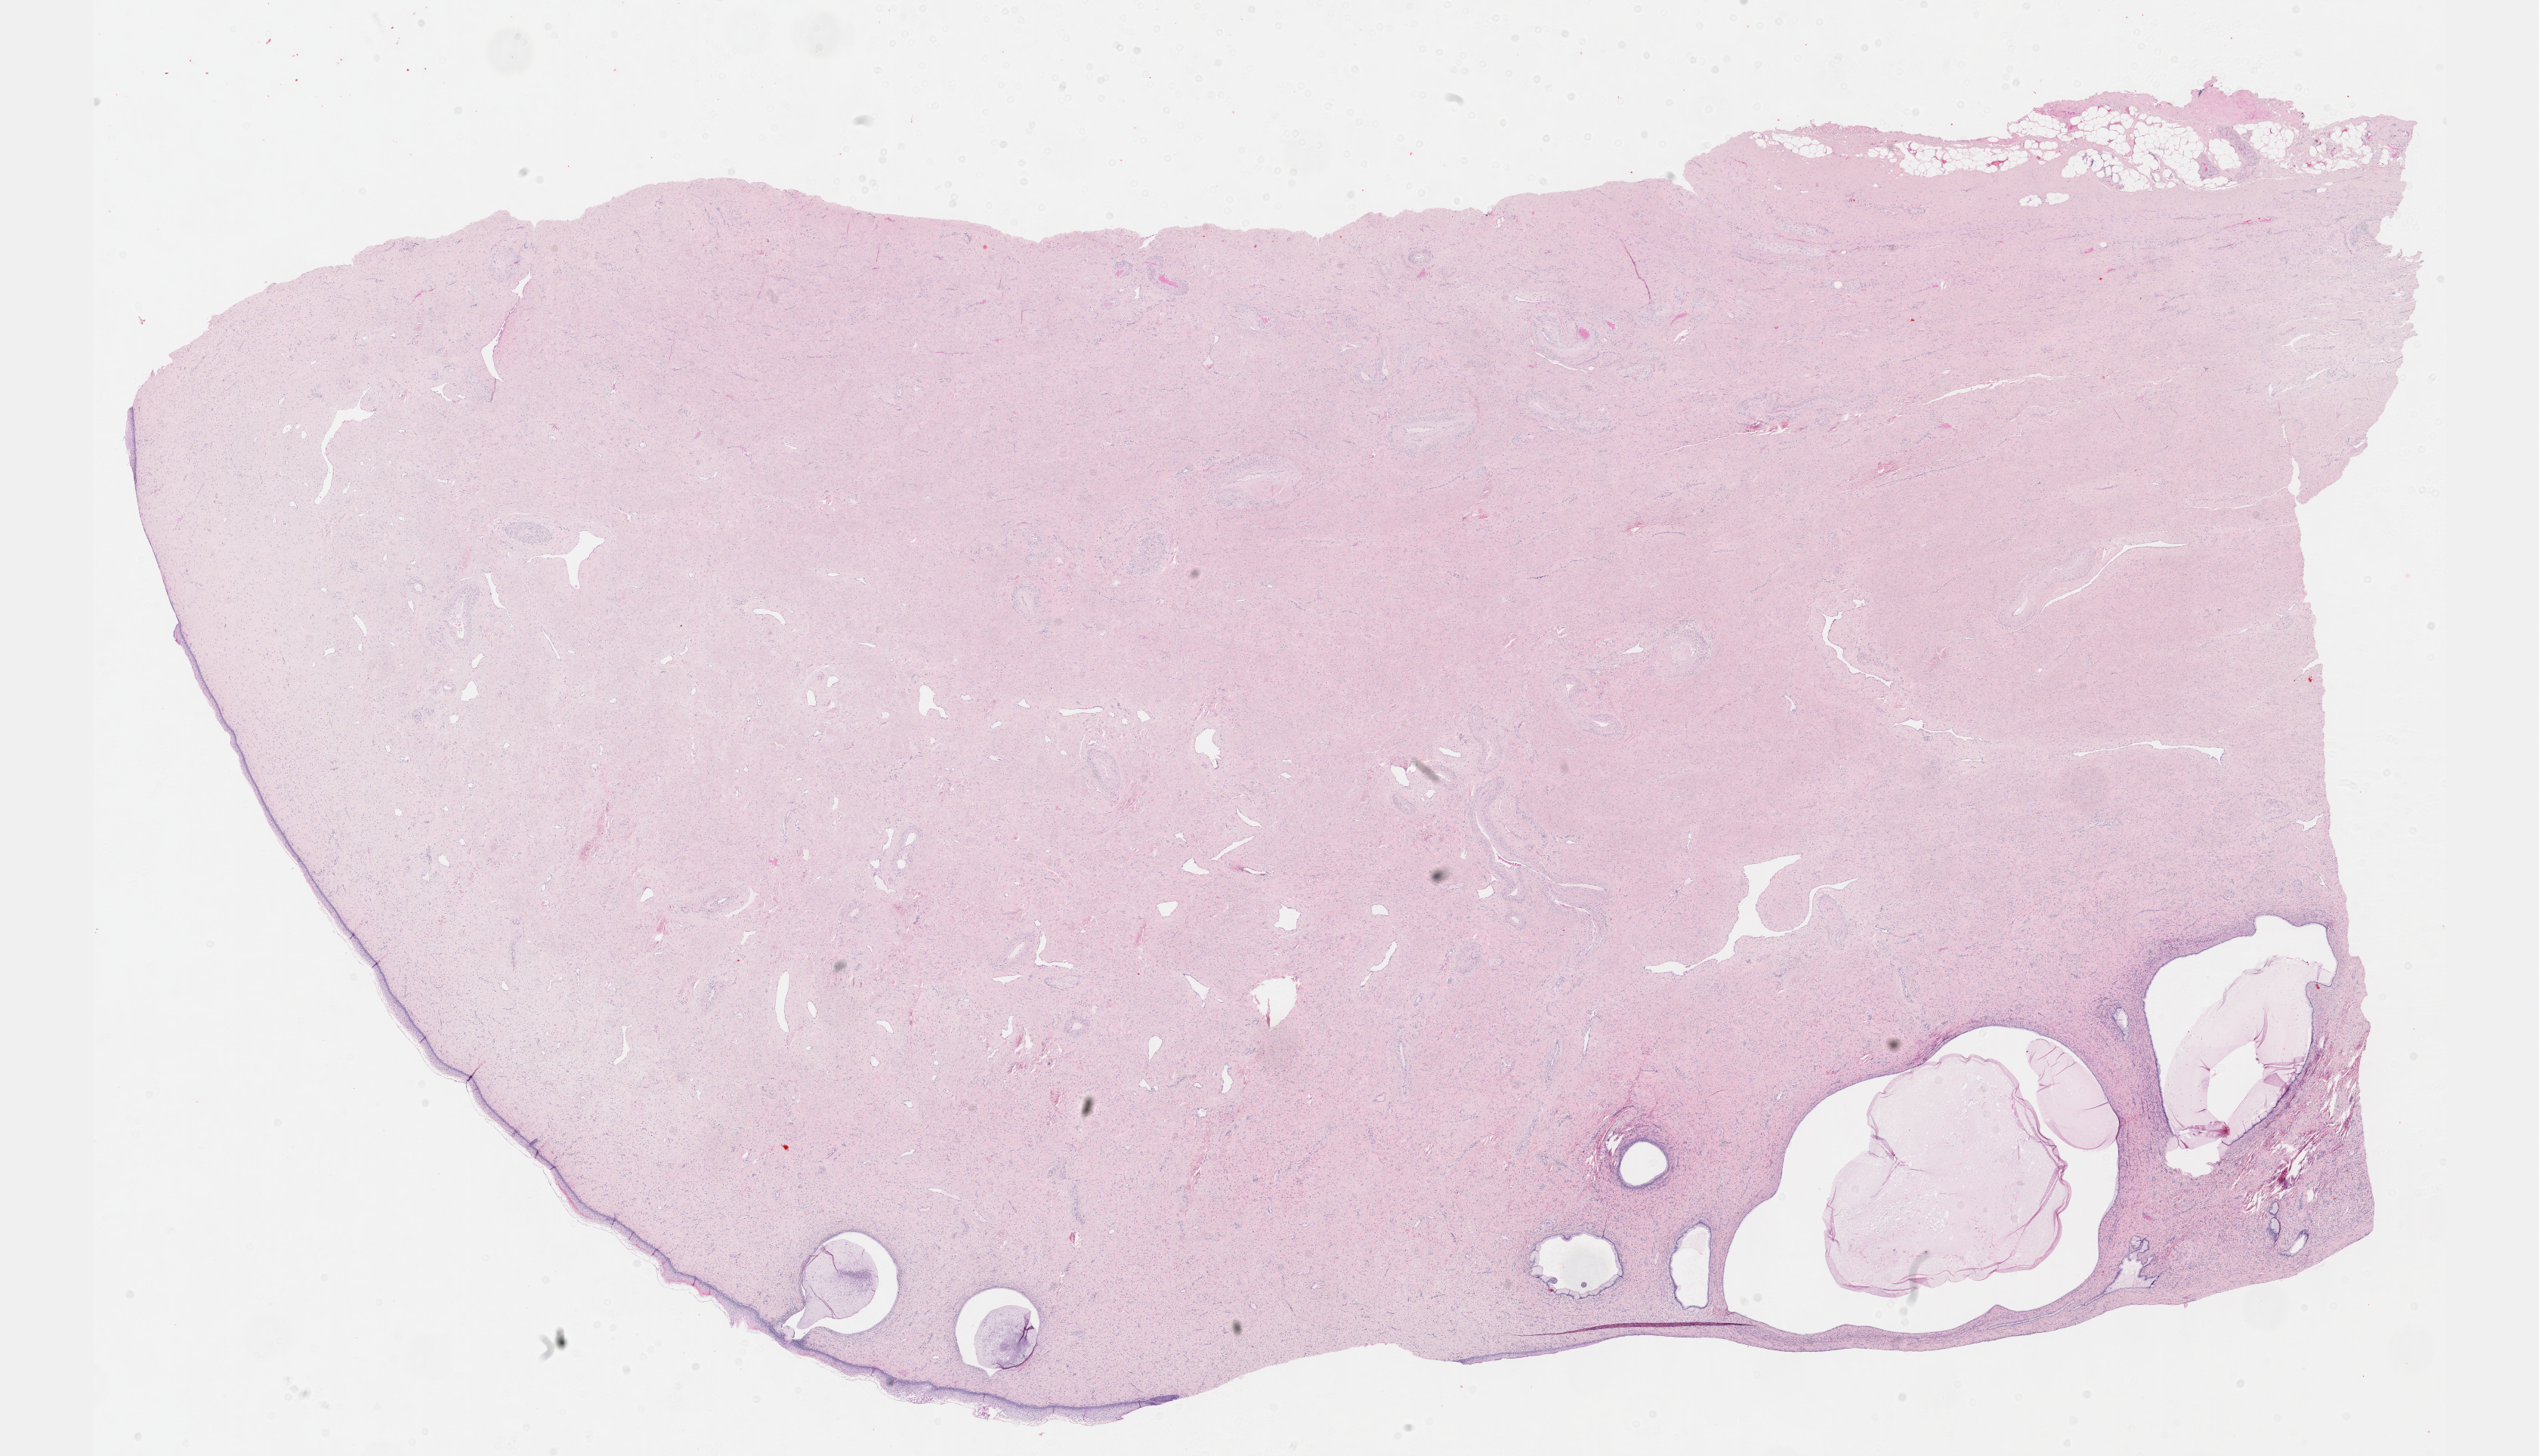
Whole-slide histology image, Hematoxylin and eosin (H&E) stained — low-resolution overview of the scanned area, about 27.2 x 15.6 mm (acquisition: 40x scan), formalin-fixed paraffin-embedded (FFPE) diagnostic section, primary tumour sample from the uterus. Patient: female, age at initial diagnosis 73 years. Histologic grade: G3 (poorly differentiated).
Pathologic diagnosis: Serous surface papillary carcinoma (endometrium). FIGO stage: IA.